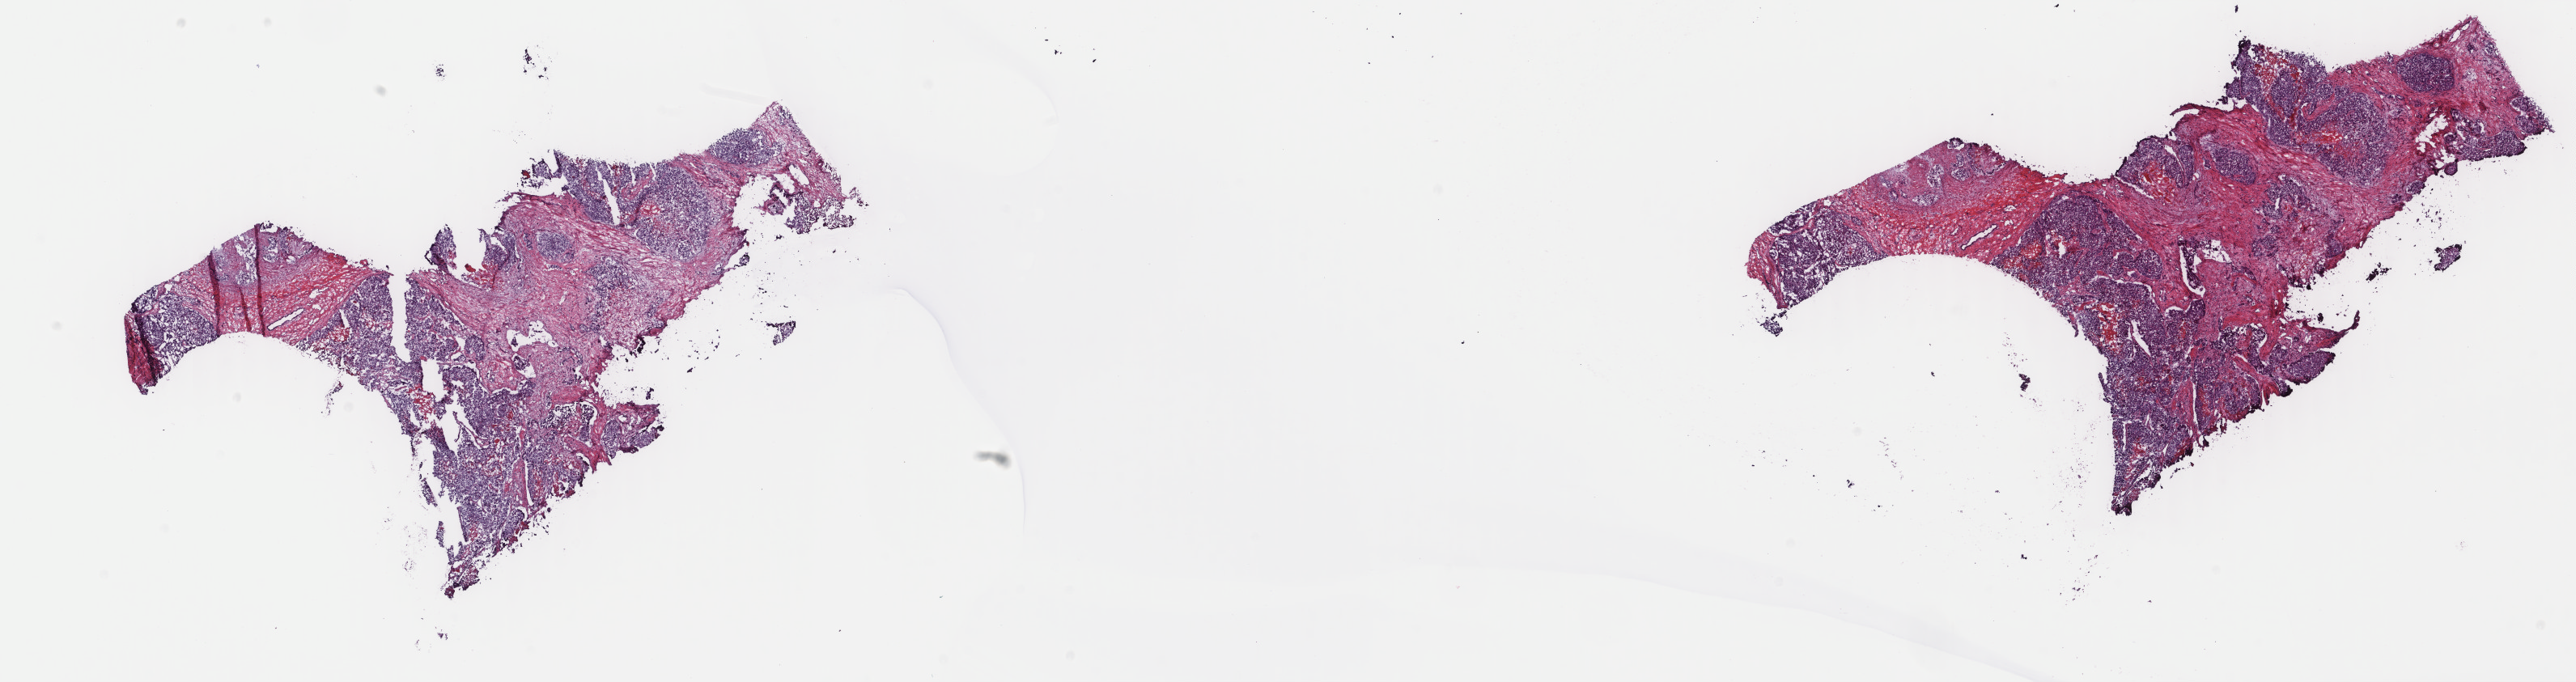
Whole-slide histology image, H&E-stained — whole scanned area (about 25.3 x 6.7 mm, from a 40x scan) shown as a low-resolution overview. Frozen section. Sample: primary tumour, liver. Male patient; age at initial diagnosis 73 years. Histologic grade: G3 (poorly differentiated). Pathologist review of this section (percent, as recorded): tumour cells 65%, tumour nuclei 70%, normal cells 0%, stromal cells 35%, necrosis 0%. Infiltration values recorded for this section: lymphocyte infiltration 0%, monocyte infiltration 0%, neutrophil infiltration 0%.
Pathologic diagnosis: Hepatocellular carcinoma, NOS. AJCC pathologic stage: II.